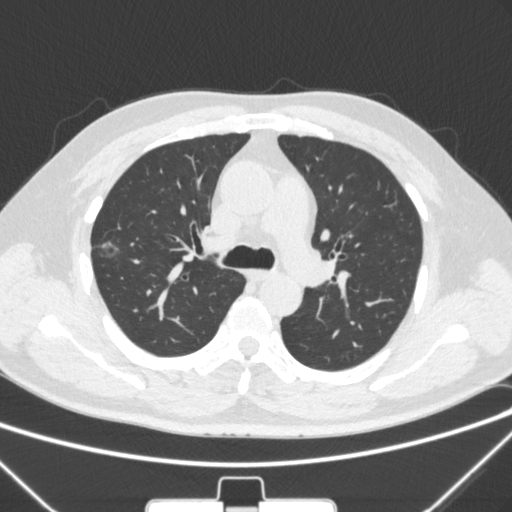
Chest CT, one axial slice; slice 203 of 320 in the series (ordered by position); 120 kVp; lung window (W 1500 / L -600 HU); 1 mm slice thickness; 512 × 512 image matrix, field of view 350 × 350 mm. Patient: male, 58 years. Case-level facts recorded for this patient, not image findings: clinical TNM (as recorded): T1c N0 M0; histopathological grade: G2.
Outlined on this slice (bounding box drawn by a radiologist):
- lung tumour (recorded histology: adenocarcinoma): bounding box [x1, y1, x2, y2] px = [92, 232, 132, 271]